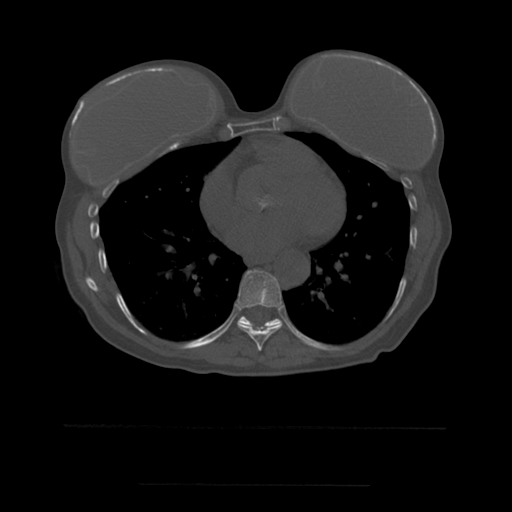
CT including the spine, one axial slice; bone window (W 1800 / L 400 HU); 1.25 mm slice thickness; 512 × 512 image matrix. Patient age 58 years. From the clinical record (not read from this slice): primary cancer: lung.
Outlined on this slice (semi-automatically segmented with operator editing):
- T8 vertebra: bounding box [x1, y1, x2, y2] px = [237, 270, 283, 351]
- T9 vertebra: [214, 307, 280, 341]